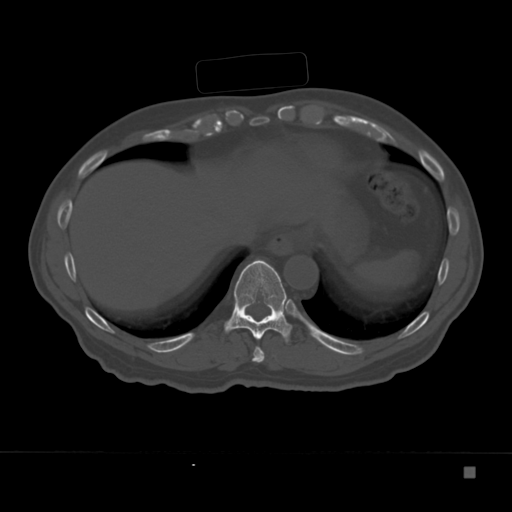
CT including the spine, one axial slice. Slice 173 of 332 in the series (ordered by position). Reconstruction kernel Br40s. 120 kVp. Bone window (W 1800 / L 400 HU). 1.5 mm slice thickness. 512 × 512 image matrix, field of view 389 × 389 mm. Male patient, age 72 years. From the clinical record (not read from this slice): primary cancer: skeletal.
Structures marked on this image (semi-automatic segmentation, software-assisted and operator-edited):
- T10 vertebra: bounding box <224,260,292,342> (left, top, right, bottom; pixels)
- T9 vertebra: <252,346,265,363>